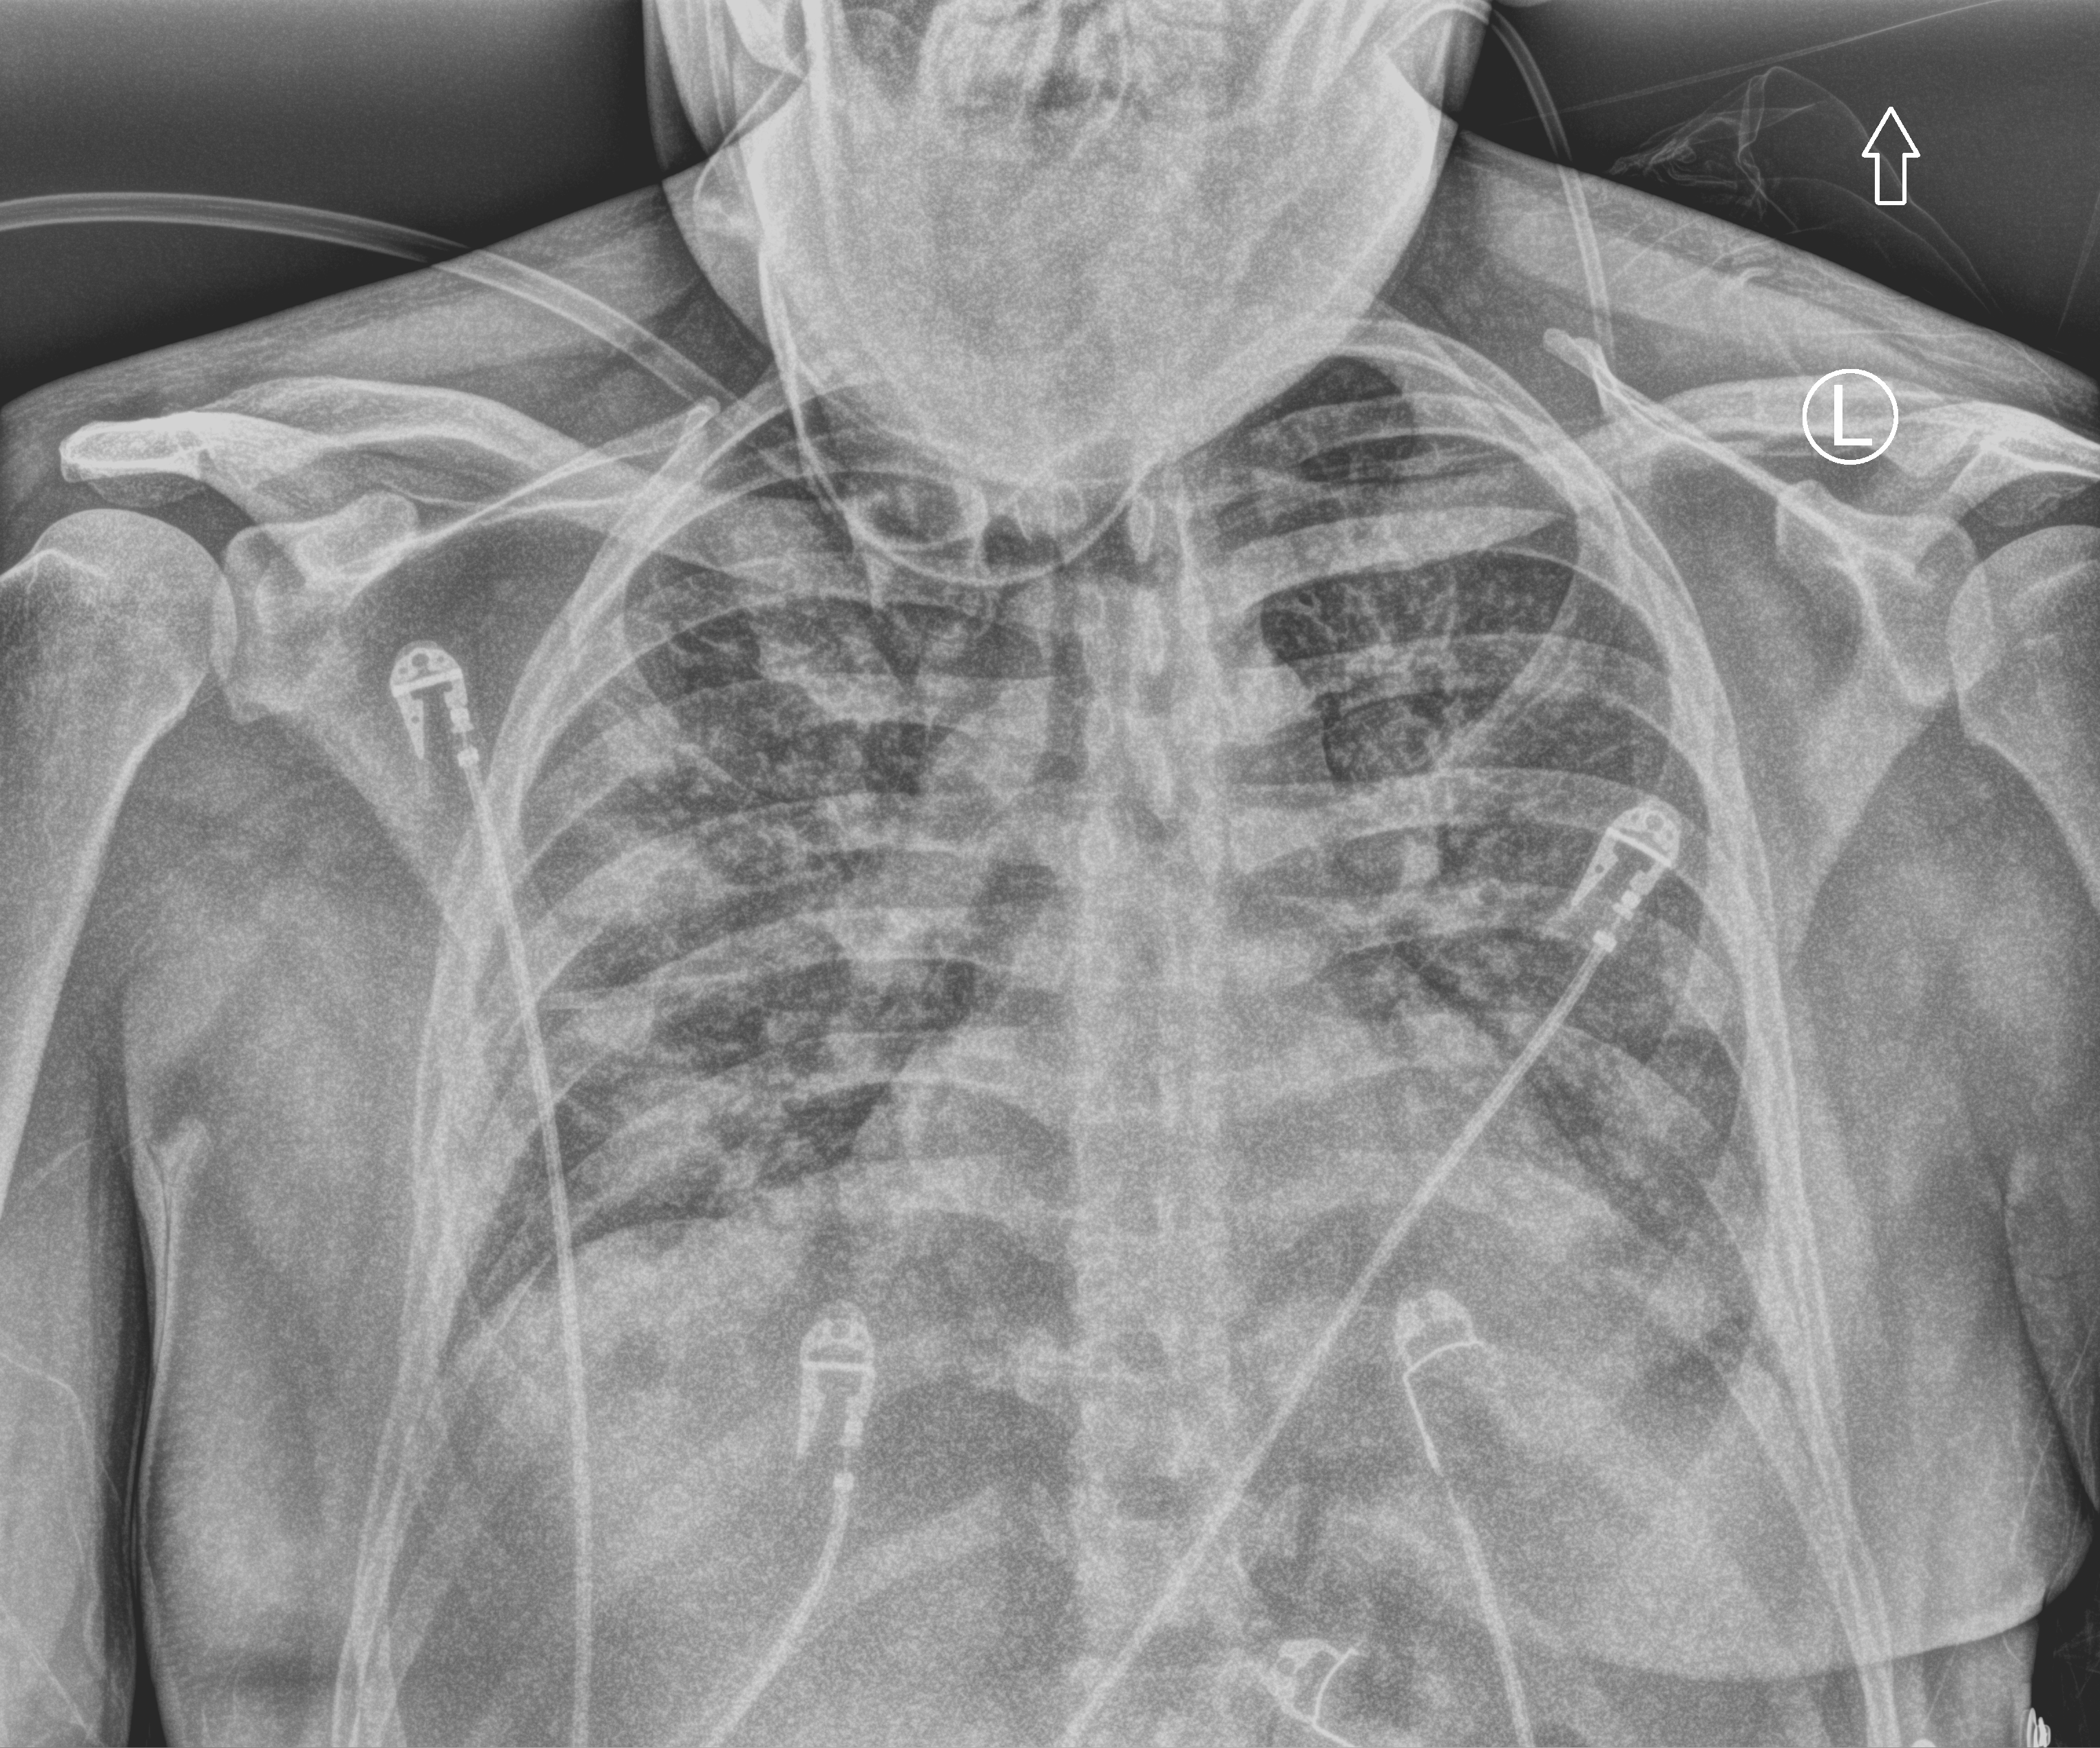
Bedside chest radiograph (computed radiography). Male patient hospitalised with COVID-19, age 18–59 years.
Admission-level facts for this patient (not findings on this image; timing relative to this image not recorded):
- mechanically ventilated during this hospital stay: yes